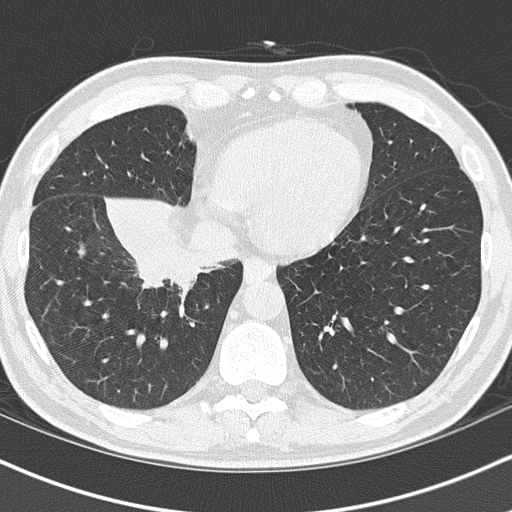
Low-dose screening chest CT, one axial slice. Position 36 of 151 along the scan axis. Reconstruction kernel B50f. Lung window (W 1500 / L -600 HU). 2 mm slice thickness. 512 × 512 image matrix.
Annotated regions visible in this slice (outlined manually by an expert reader):
- lesion 1 (tumor, hilum of right lung): bounding box (x1, y1, x2, y2) in pixels: (134, 227, 202, 283)